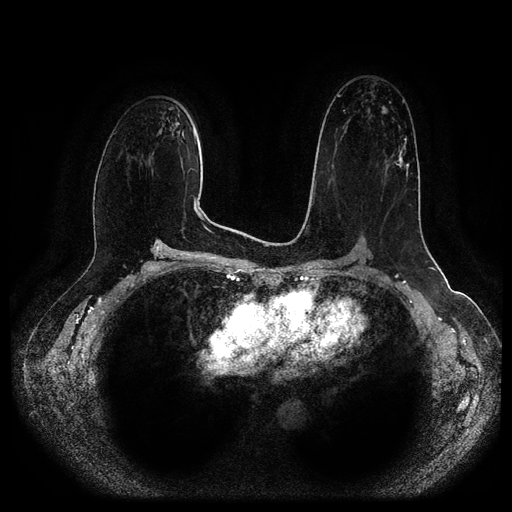
Breast MRI (dynamic contrast-enhanced, multi-phase), one axial slice. Slice 61 of 116 in the series (ordered by position). Dynamic contrast-enhanced series, time point 2 of 5 at this slice position (early post-contrast). 1.5 T. TE 2.6 ms, TR 5.2 ms. 2 mm slice thickness. 512 × 512 image matrix, field of view 380 × 380 mm. Female patient, age 57 years.
Outlined on this slice (semi-automatically segmented with operator editing):
- breast lesion (labelled 'tumour' in the annotation; benign lesions carry a separate 'benign' label): bounding box [x1, y1, x2, y2] px = [388, 136, 412, 177]